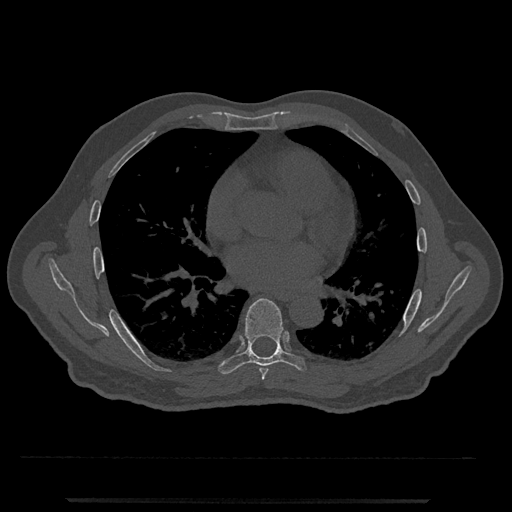
CT including the spine, one axial slice; slice 693 of 797 in the series (ordered by position); reconstruction kernel Br40s/3; bone window (W 1800 / L 400 HU); 0.5 mm slice thickness; 512 × 512 image matrix, field of view 419 × 419 mm. Patient: male, 63 years. Case-level facts recorded for this patient, not image findings: primary cancer: prostate.
Structures marked on this image (semi-automatically segmented with operator editing):
- T6 vertebra: bounding box [x1, y1, x2, y2] px = [259, 368, 268, 380]
- T7 vertebra: [218, 298, 306, 375]